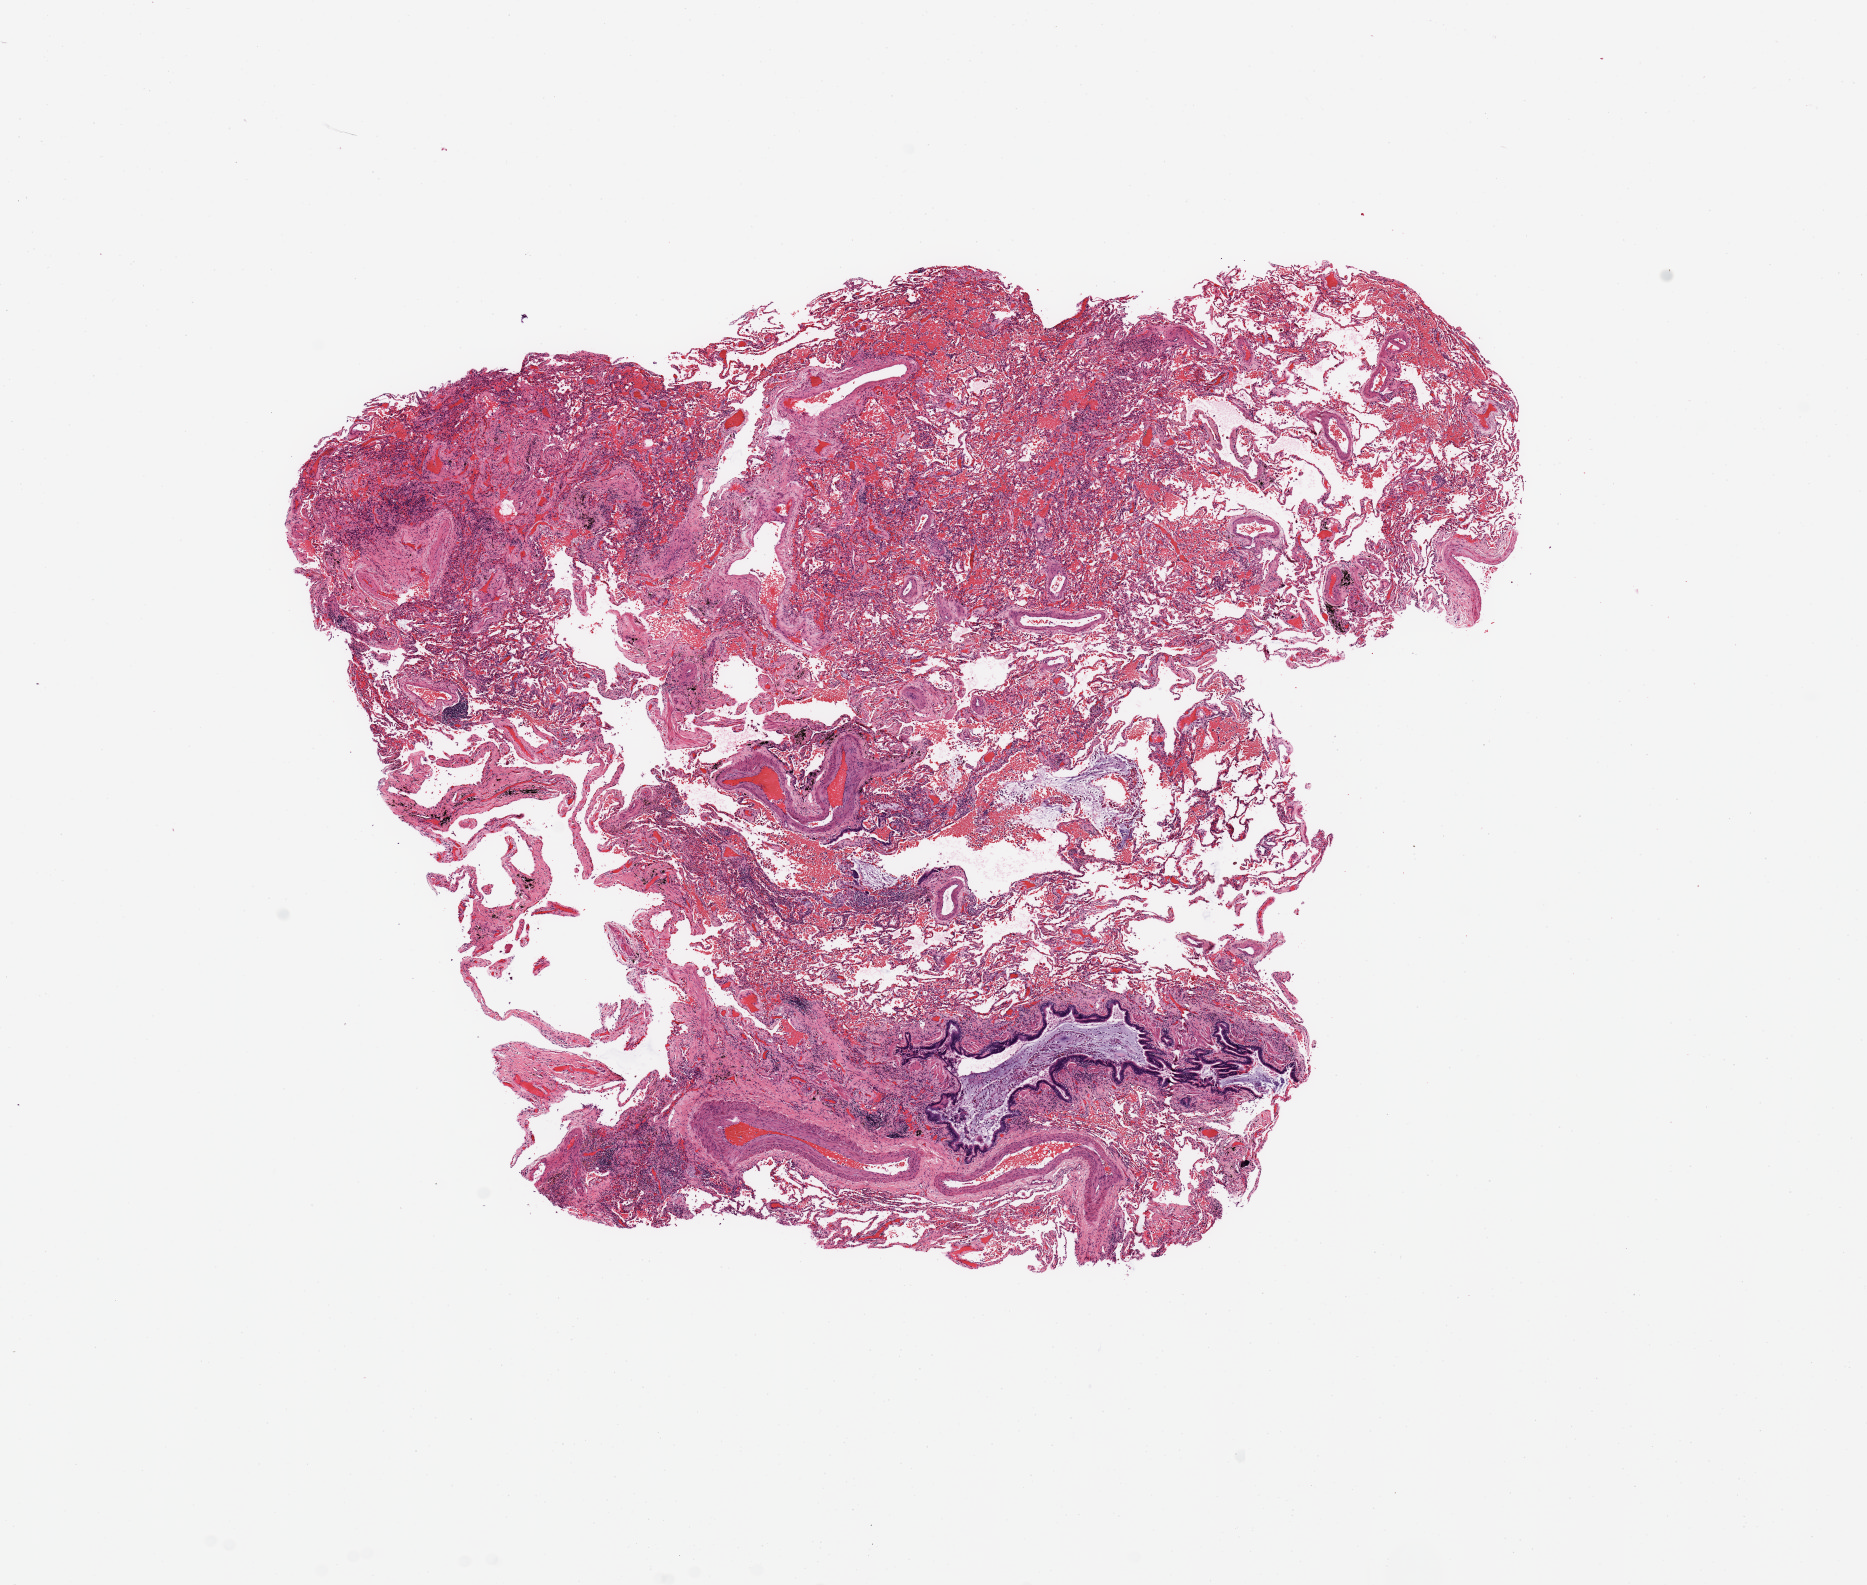
Digitized H&E-stained tissue section (whole slide), low-resolution overview of the scanned area, about 14.8 x 12.5 mm (from a 20x scan), normal (non-tumour) tissue sample, sampled site: lung. Male, 71 y/o.
This section: normal (non-tumour) tissue from the same patient. Patient diagnosis: Squamous cell carcinoma, NOS.